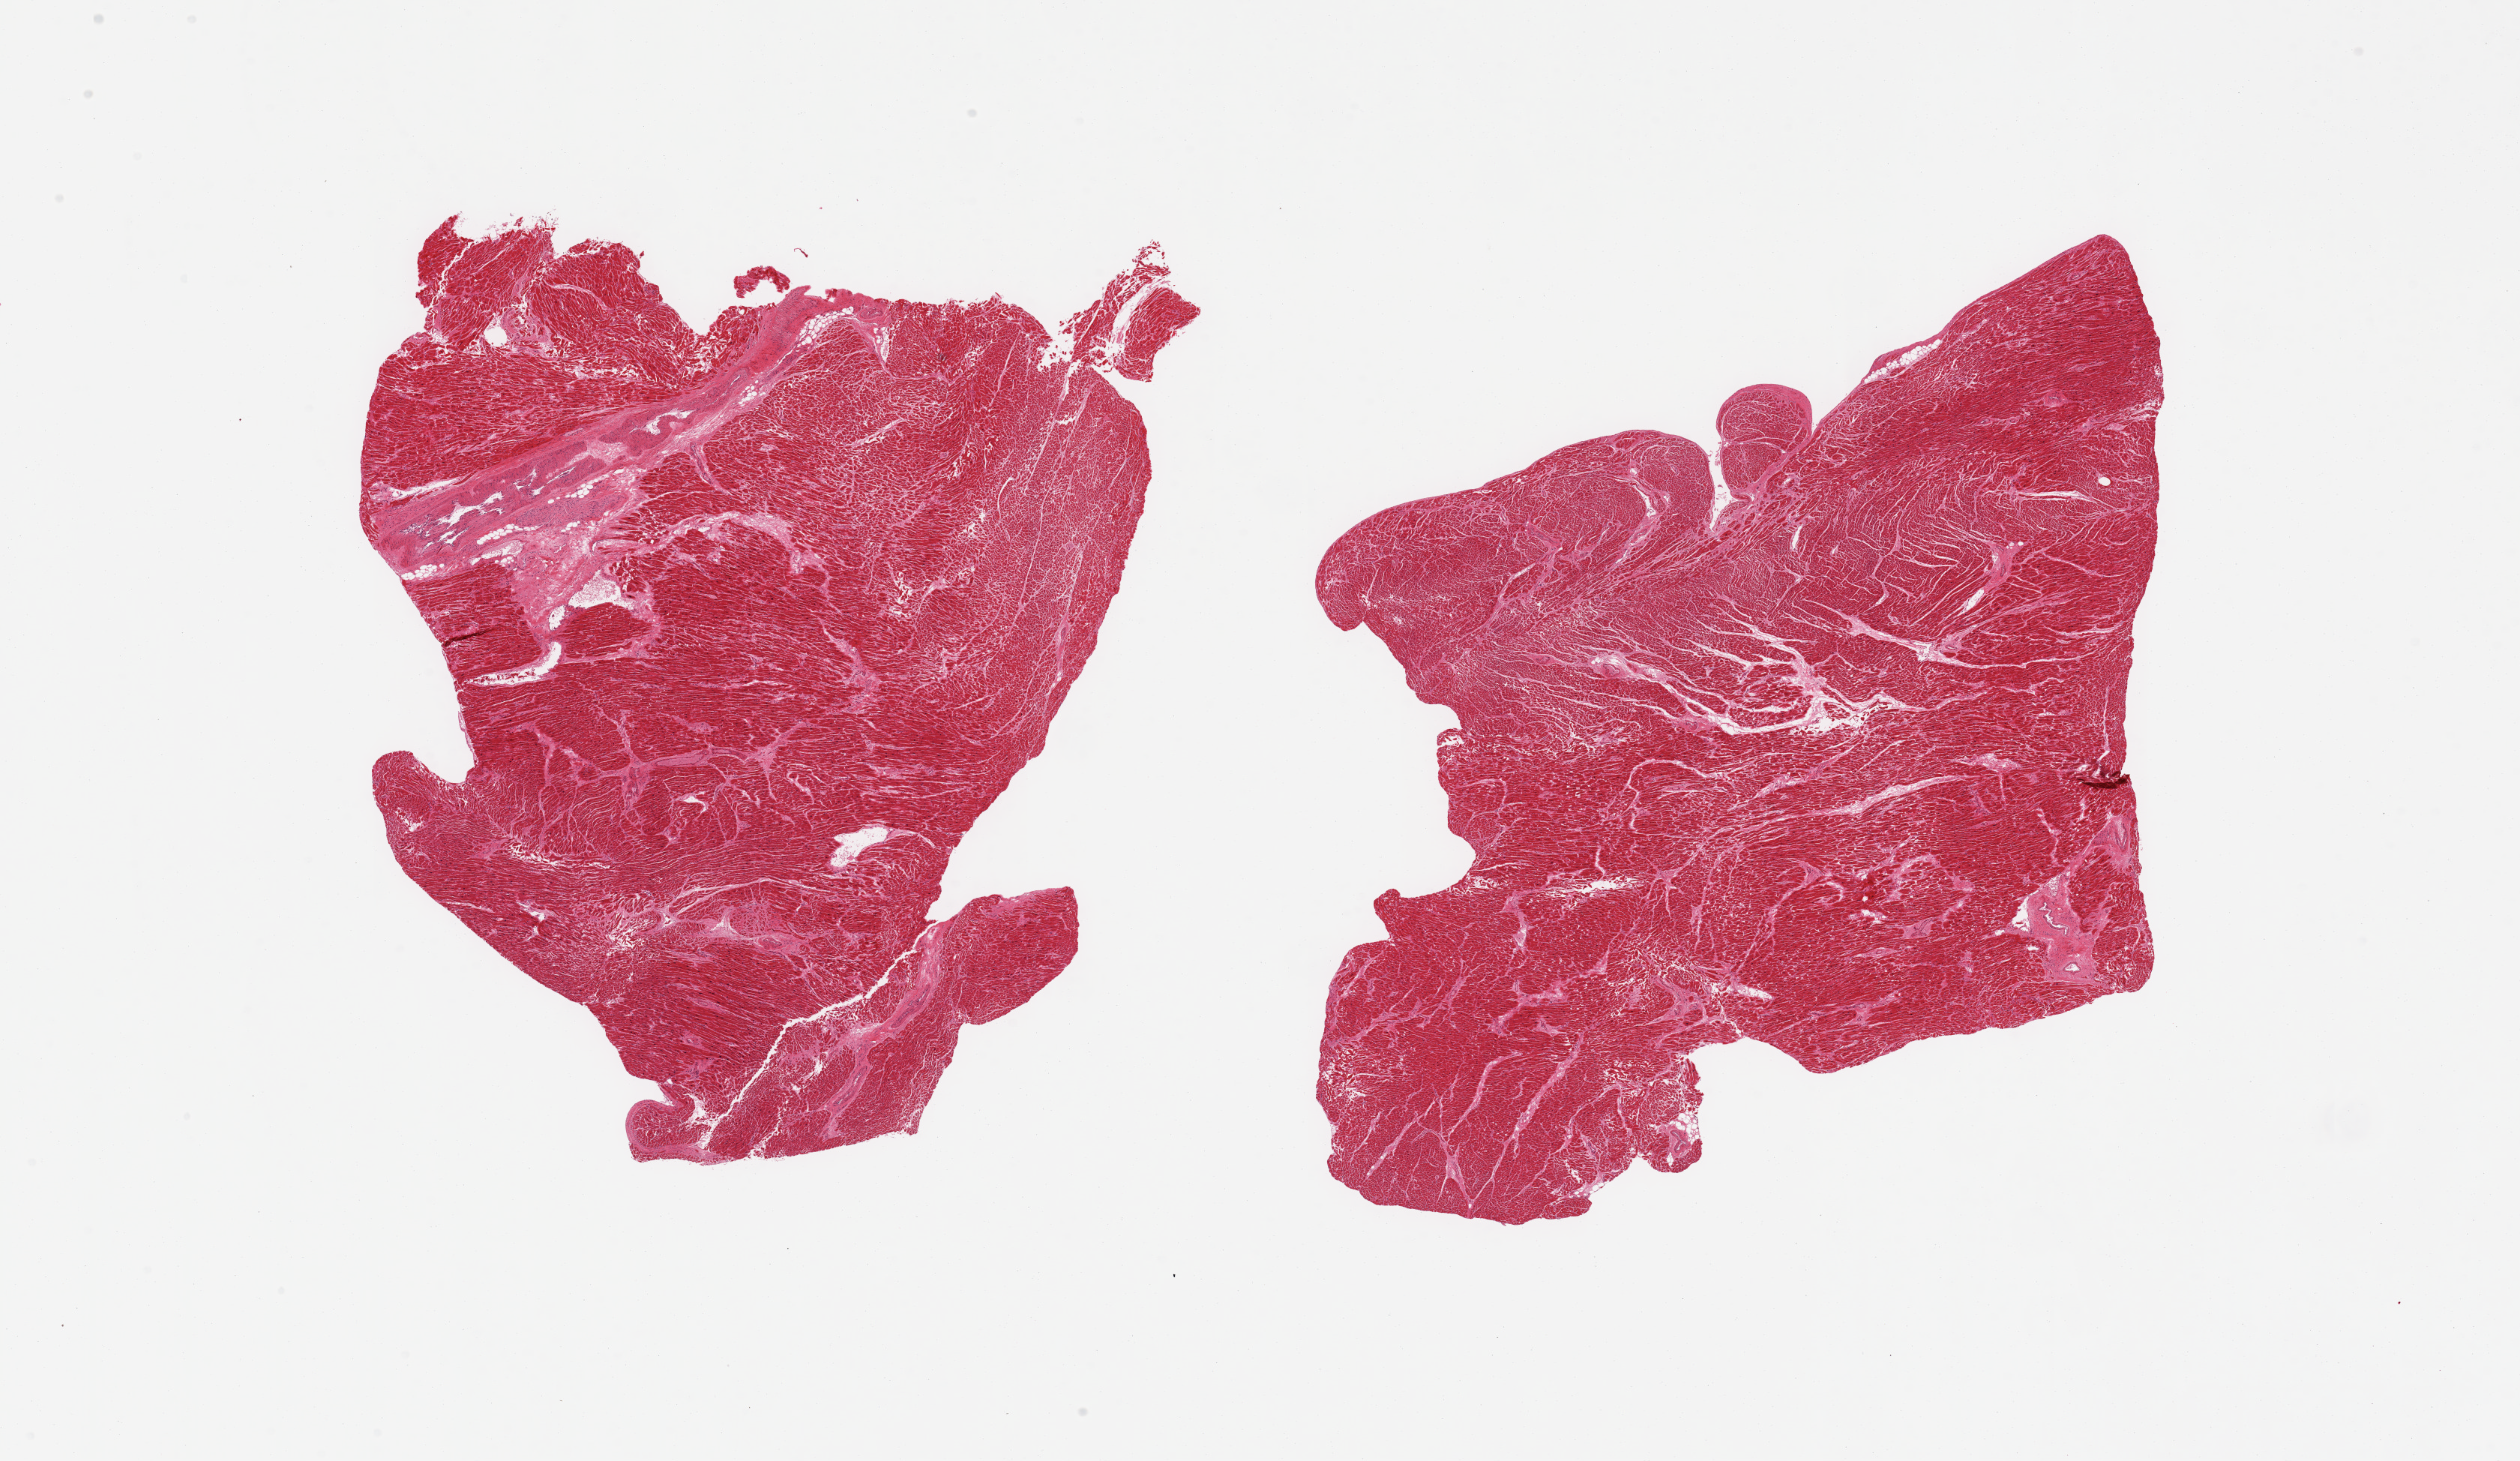
Digitized haematoxylin and eosin-stained section, shown as a low-resolution overview of the whole scanned area (about 26.6 x 15.4 mm, acquisition: 20x scan); PAXgene-fixed paraffin-embedded (PFPE) section; section of heart (target tissue); tissue donor sample.
Pathologist's review note for this sample: 2 pieces; prominent myofiber fragmentation.